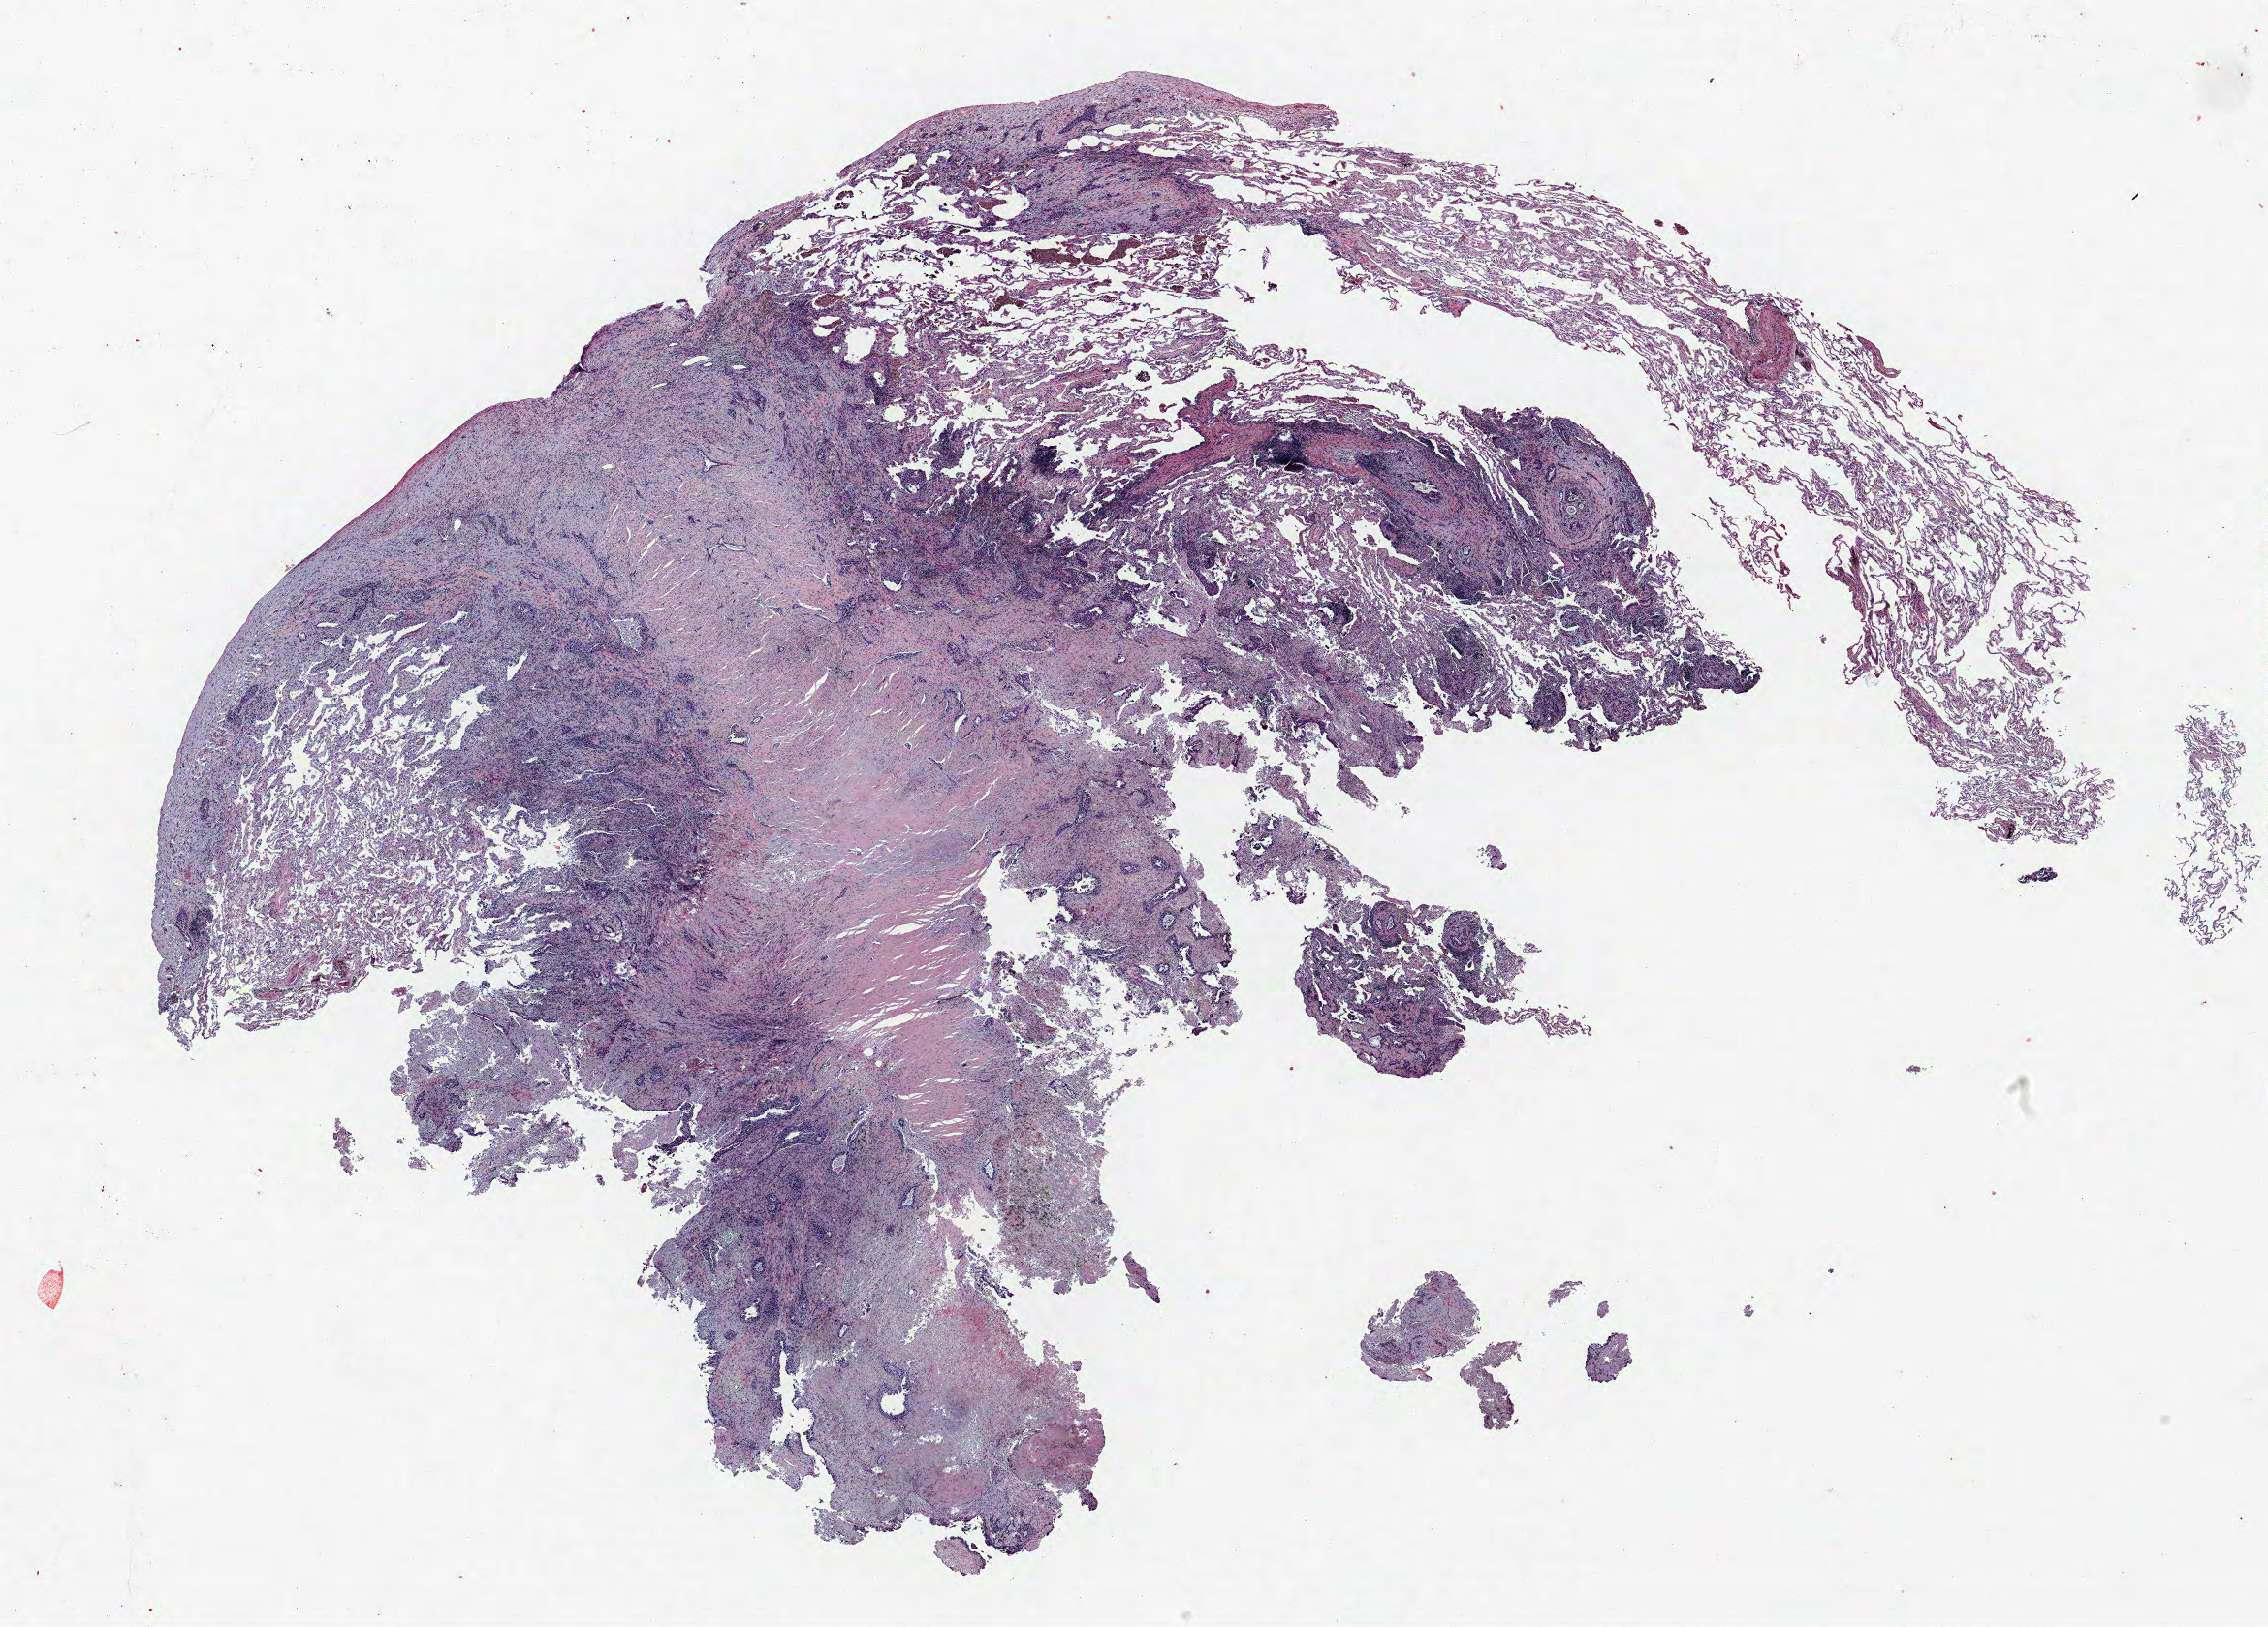
H&E-stained whole-slide image — shown as a low-resolution overview of the whole scanned area (about 18.7 x 13.4 mm, slide scanned at 40x), FFPE section, lung tissue. Male, age 59 at enrolment.
Participant's lung-cancer diagnosis: Non-small cell carcinoma (ICD-O-3 8046/3).